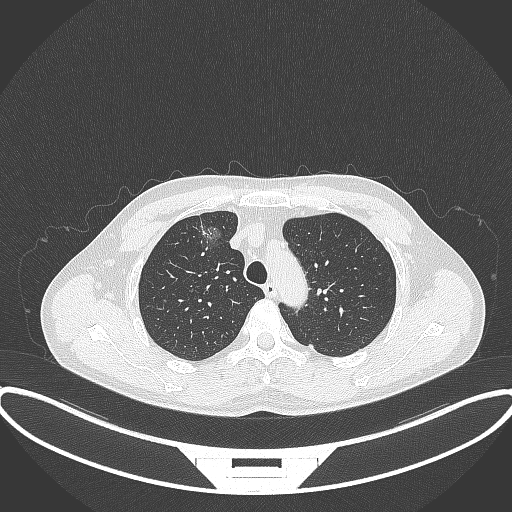
Chest CT, one axial slice; position 281 of 395 along the scan axis; 120 kVp; lung window (W 1500 / L -600 HU); 1 mm slice thickness; 512 × 512 image matrix, field of view 424 × 424 mm. Patient: male, 60 years. Case-level facts recorded for this patient, not image findings: clinical TNM (as recorded): T1c N0 M0.
Structures marked on this image (rectangle marked by the reading radiologist):
- lung tumour (recorded histology: adenocarcinoma): bounding box <194,218,232,257> (left, top, right, bottom; pixels)